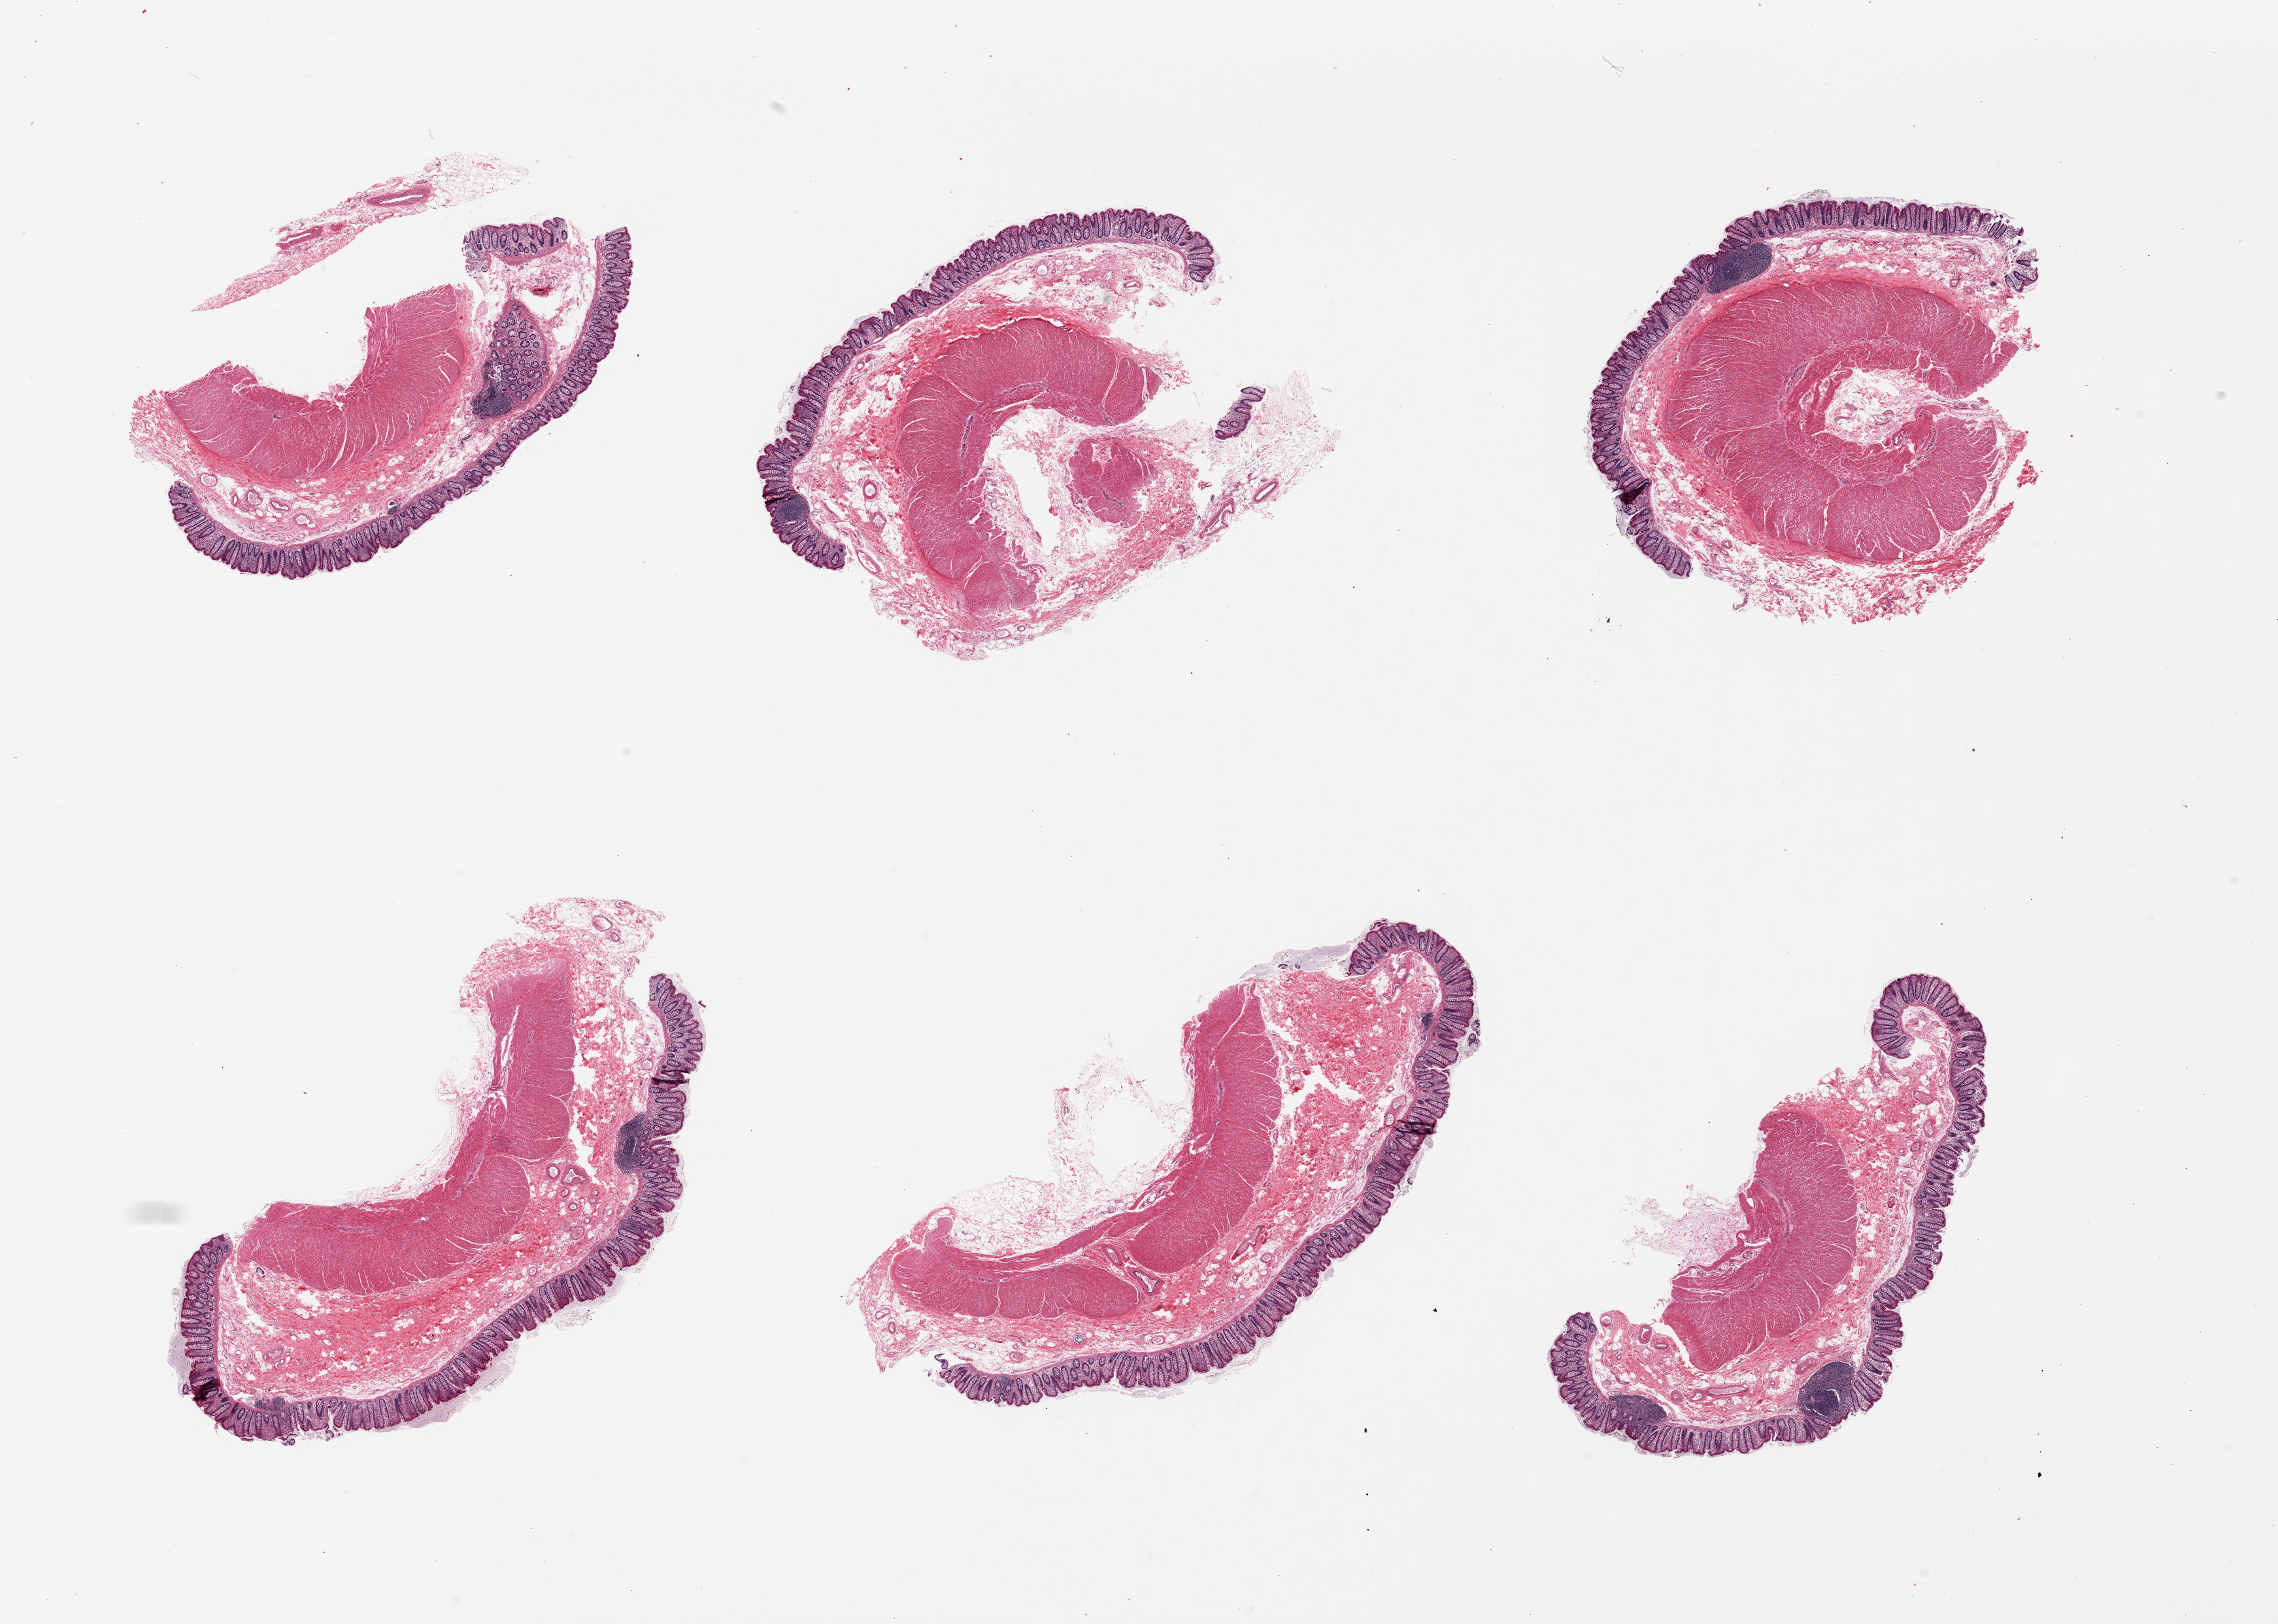
Digitized hematoxylin and eosin (H&E)-stained section, brightfield — shown as a low-resolution overview of the whole scanned area (about 27.6 x 19.7 mm); PAXgene-fixed, paraffin-embedded tissue; section of sigmoid colon (target tissue); tissue donor sample. Male donor.
- pathologist's review note for this sample: 6 pieces, well preserved, ~50% muscularis, the rest fat and mucosa, ~10% thickness